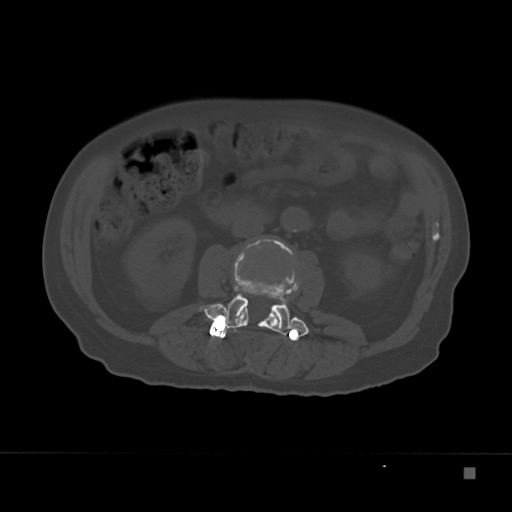
CT including the spine, one axial slice; slice 77 of 332 in the series (ordered by position); reconstruction kernel Br40s; 120 kVp; bone window (W 1800 / L 400 HU); 512 × 512 image matrix. Patient: male, 72 years. From the clinical record (not read from this slice): primary cancer: skeletal.
Structures marked on this image (semi-automatic segmentation, software-assisted and operator-edited):
- L2 vertebra: bounding box (x1, y1, x2, y2) in pixels: (234, 237, 287, 328)
- L3 vertebra: (199, 266, 309, 336)